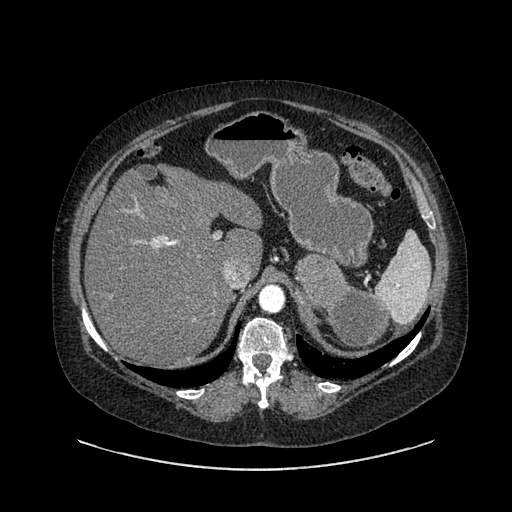
Contrast-enhanced abdominal CT, one axial slice; position 617 of 769 along the scan axis; soft-tissue window (W 400 / L 40 HU); 0.62 mm slice thickness; 512 × 512 image matrix. Female patient, age 61 years. From the clinical record (not read from this slice): diagnosis: adrenocortical carcinoma; tumour side: left adrenal; tumour size at pathology: 13 cm; Ki-67 index: 79 %; stage (as recorded): 2.
Annotated regions visible in this slice (semi-automatic segmentation, software-assisted and operator-edited):
- mass: box from (x=296, y=256) to (x=389, y=350) px